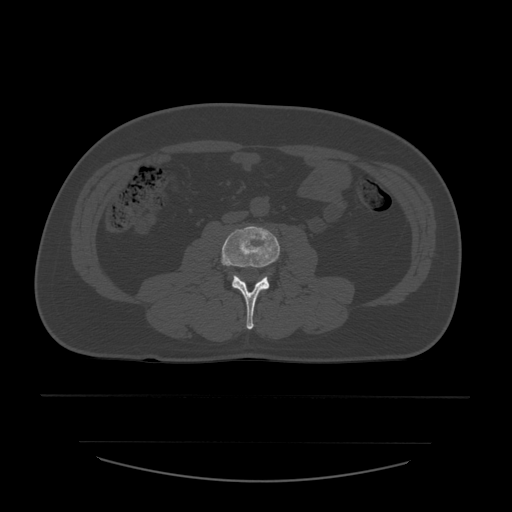
CT including the spine, one axial slice; reconstruction kernel STANDARD; bone window (W 1800 / L 400 HU); 512 × 512 image matrix, field of view 441 × 441 mm. Patient age 44 years. From the clinical record (not read from this slice): primary cancer: soft tissue sarcoma.
Structures marked on this image (semi-automatically segmented with operator editing):
- L3 vertebra: bounding box [x1, y1, x2, y2] px = [222, 226, 280, 330]